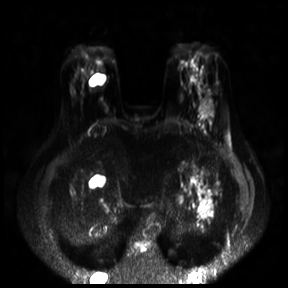
Breast MRI, one axial slice. Position 9 of 30 along the scan axis. Diffusion-weighted series; image 2 of 4 stored at this slice position (different b-values; order by instance number). 3 T. 4 mm slice thickness. 288 × 288 image matrix, field of view 360 × 360 mm. Female patient.
Annotated regions visible in this slice (expert manual segmentation):
- tumour on diffusion-weighted imaging: bounding box <198,95,213,116> (left, top, right, bottom; pixels)